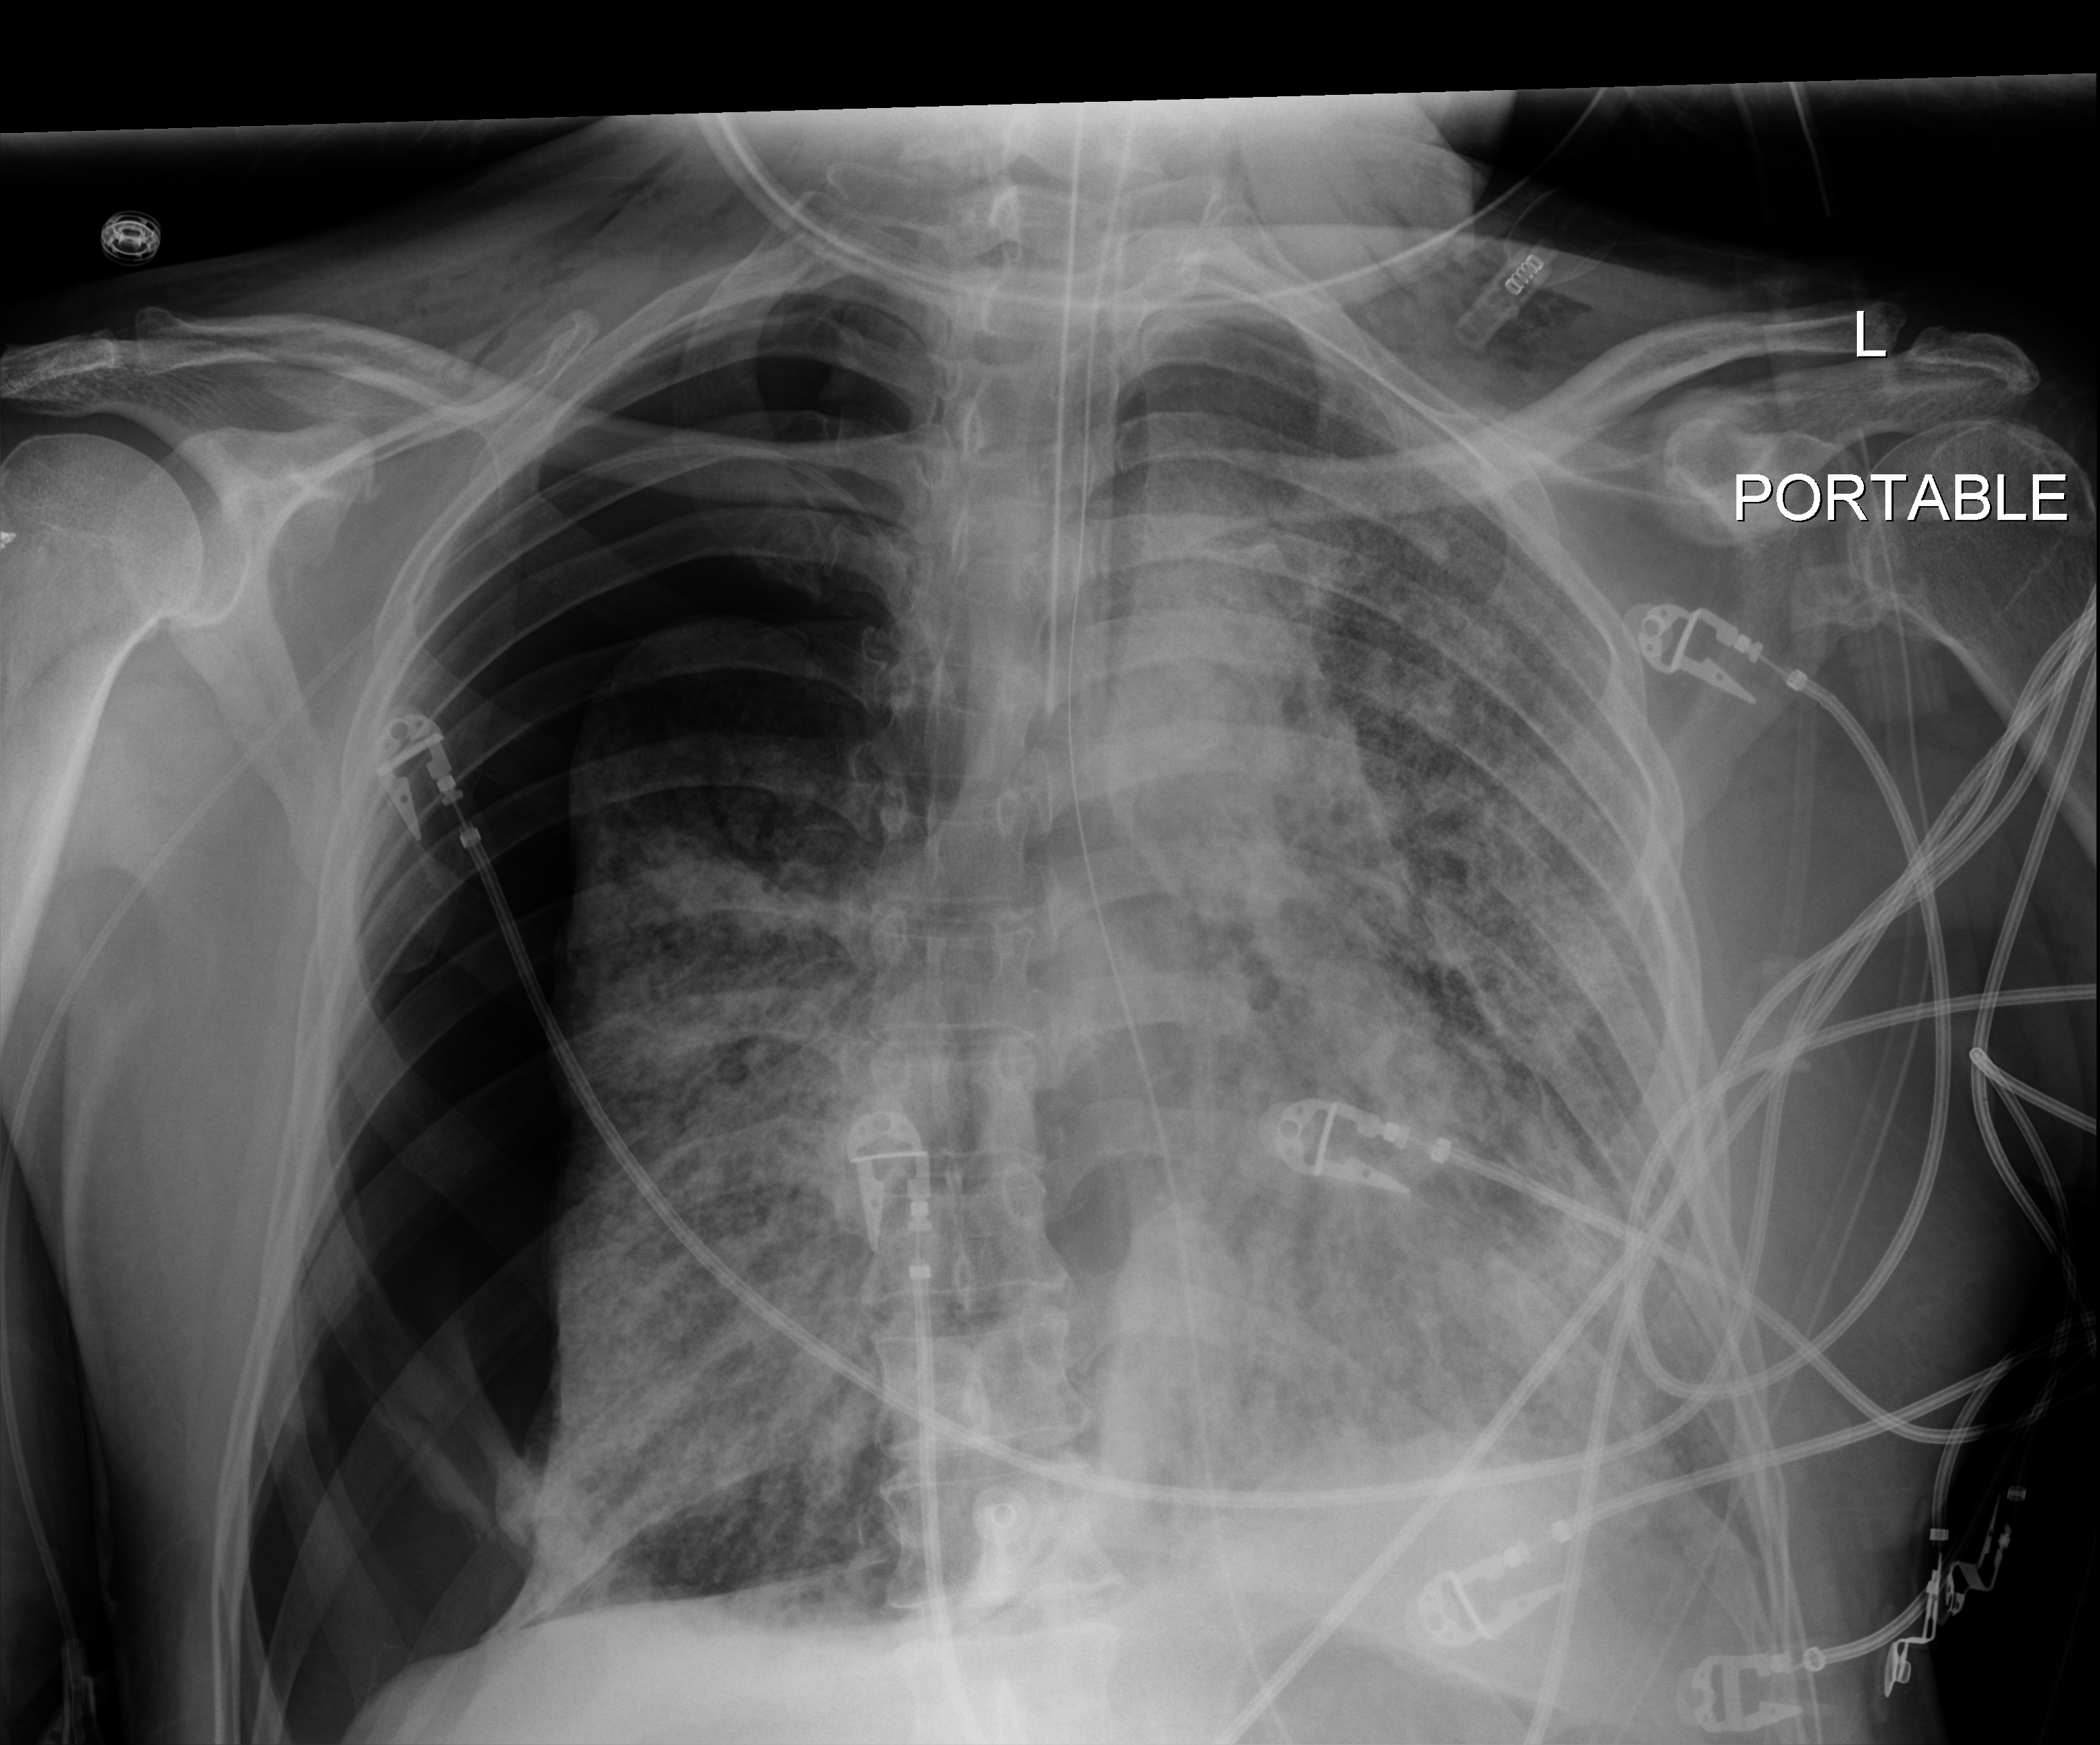
Bedside chest radiograph (digital radiography); anteroposterior (AP) projection. Patient hospitalised with COVID-19; male, aged 60–74 years.
From the hospital-stay record, not from the radiograph (when in the stay this image was taken is not recorded): admitted to intensive care during this hospital stay: yes.